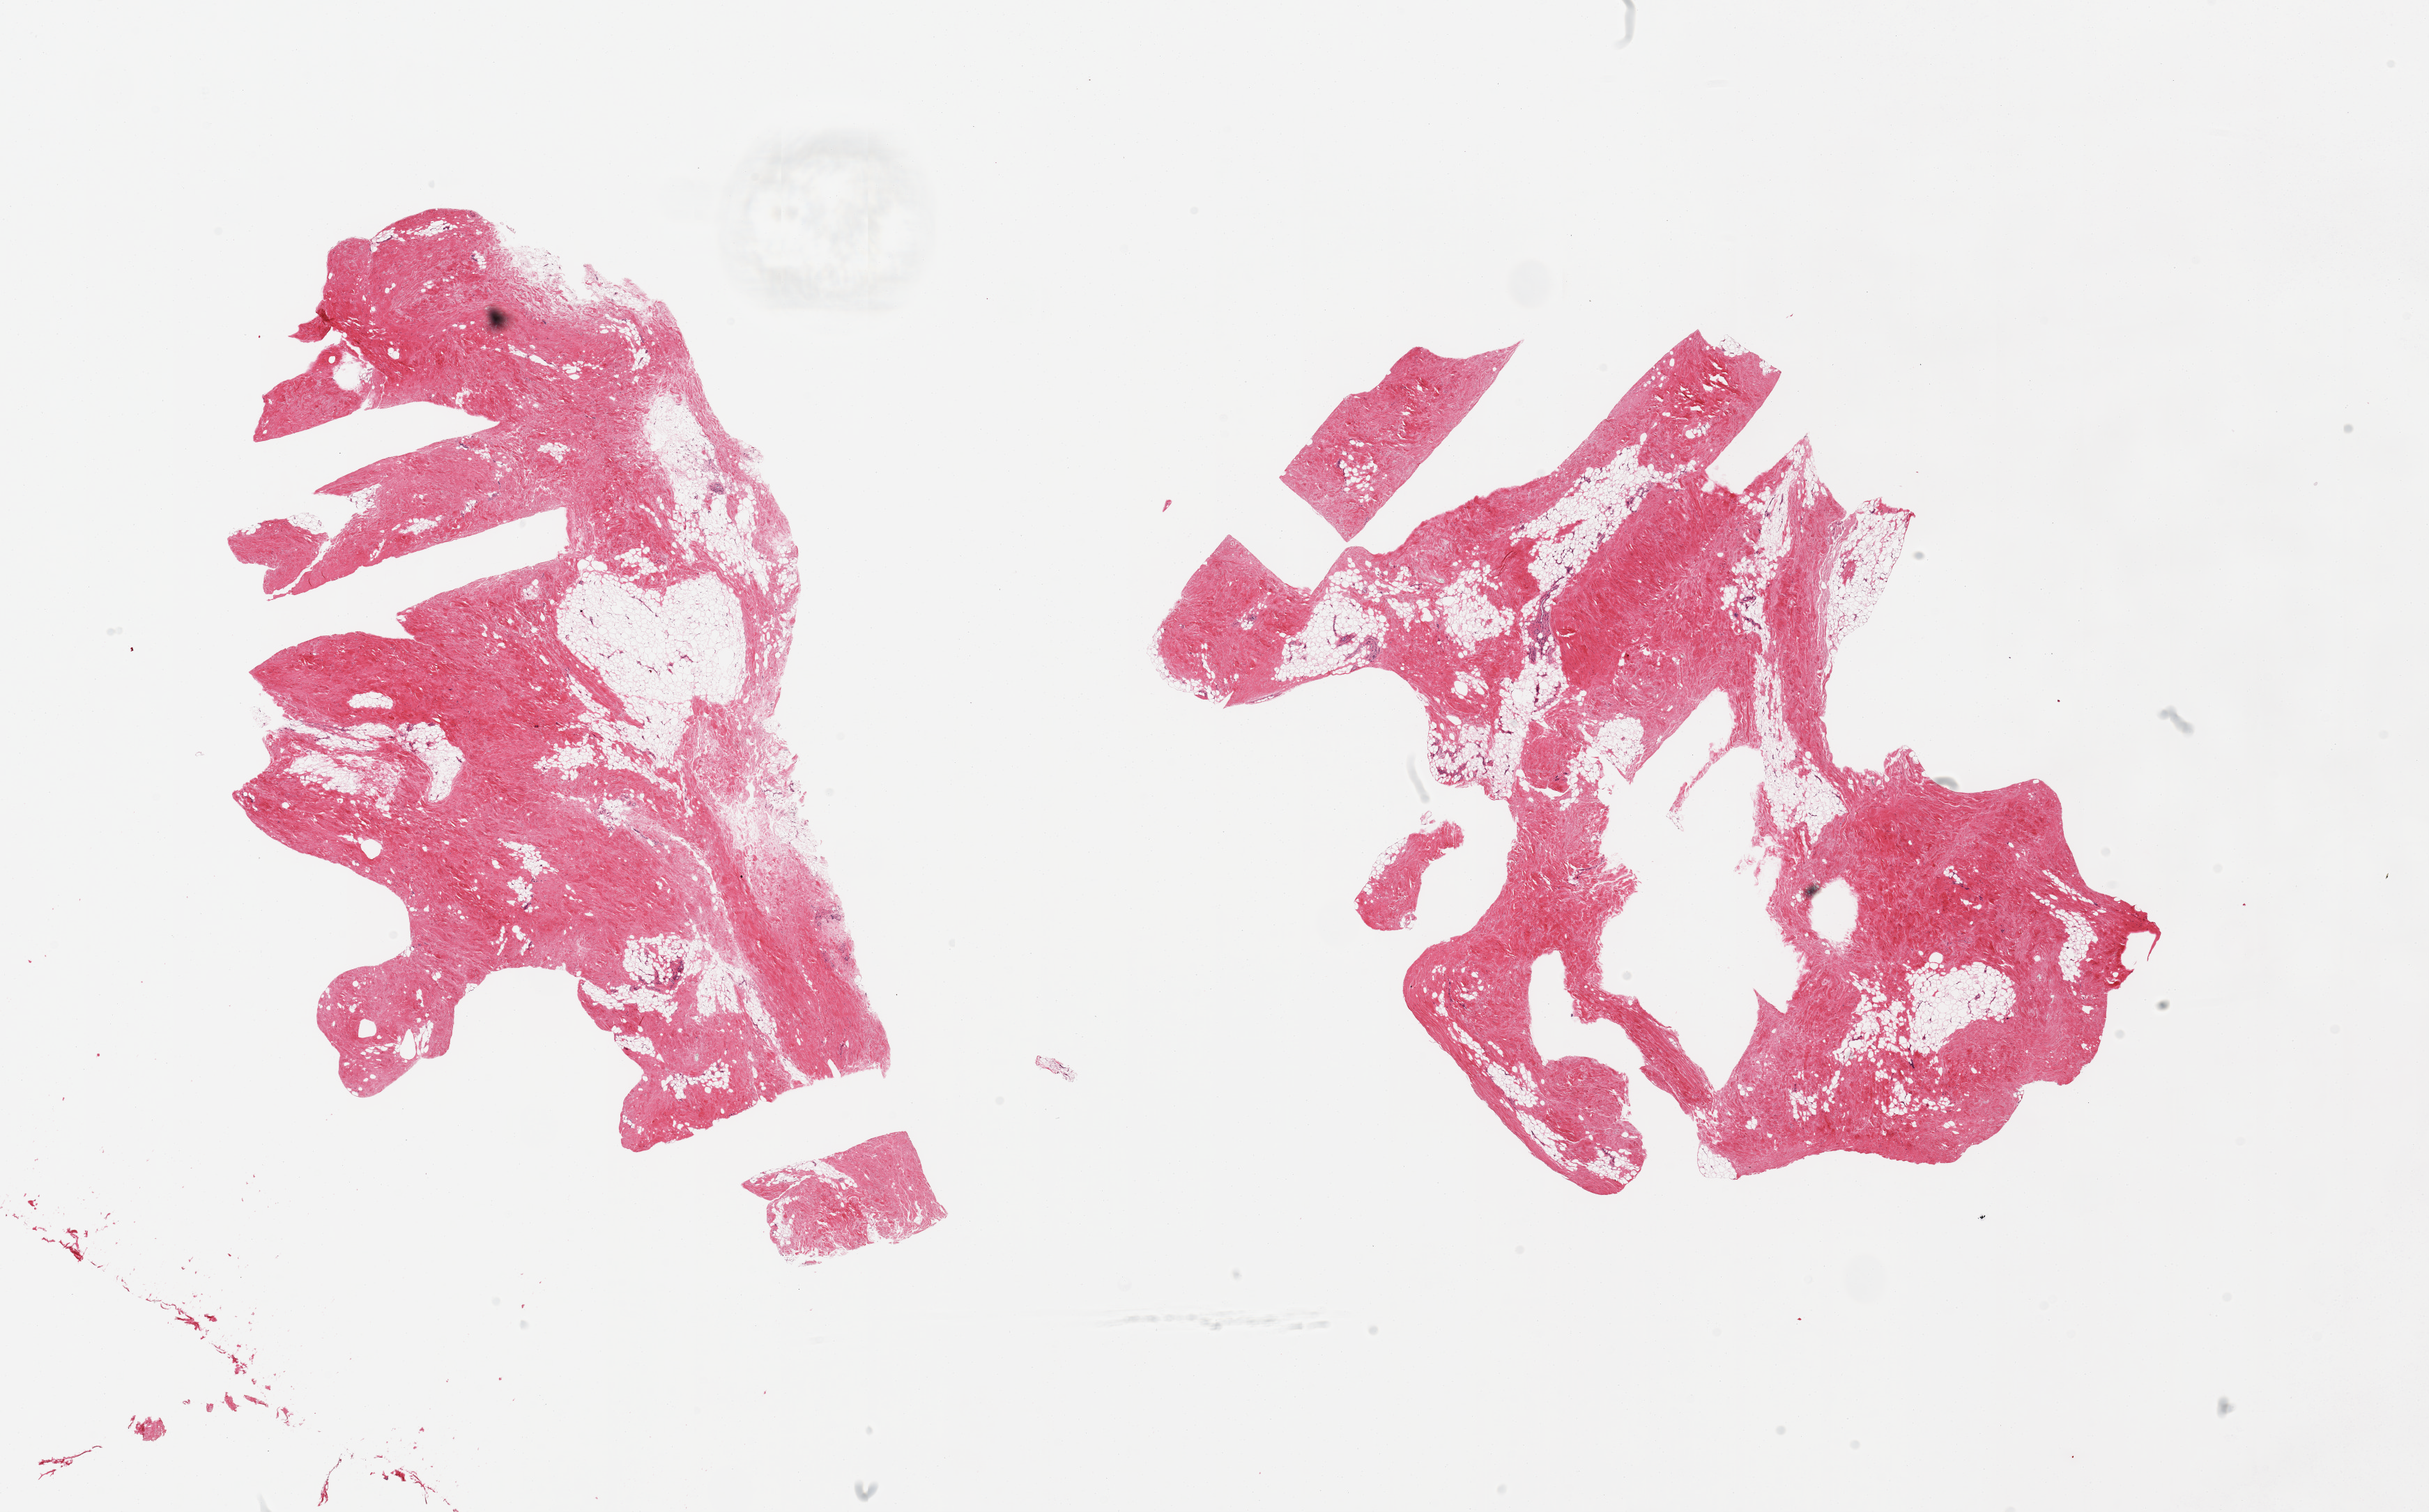
Haematoxylin and eosin whole-slide image, brightfield, shown as a low-resolution overview of the whole scanned area (about 27.6 x 17.2 mm, acquisition: 20x scan), PAXgene-fixed, paraffin-embedded tissue, sampled site (target tissue): breast, tissue donor sample. Male donor.
Reviewer comment on this tissue sample: 2 pieces, fibroadipose tissue, no ductal.